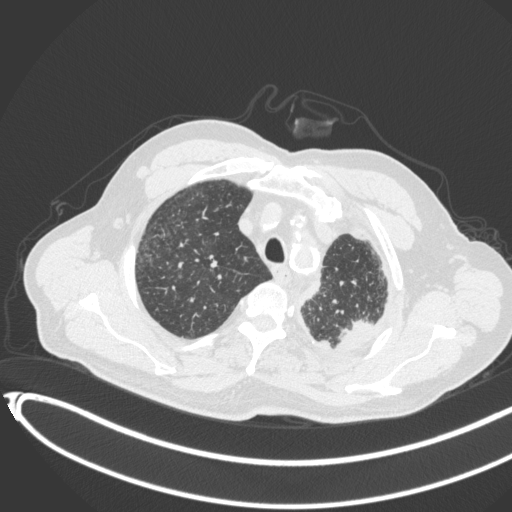
Chest CT, one axial slice; position 357 of 451 along the scan axis; 120 kVp; lung window (W 1500 / L -600 HU); 1 mm slice thickness; 512 × 512 image matrix. Patient: male, 78 years. From the clinical record (not read from this slice): clinical TNM (as recorded): T1c N0 M1.
Outlined on this slice (rectangle marked by the reading radiologist):
- lung tumour (recorded histology: adenocarcinoma): box from (x=334, y=314) to (x=383, y=359) px